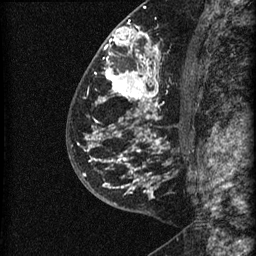
Breast MRI (dynamic contrast-enhanced), one sagittal slice. Slice 38 of 60 in the series (ordered by position). Dynamic contrast-enhanced series, image 2 of 3 at this slice position (ordered by acquisition). 1.5 T. TE 4.2 ms, TR 22.7 ms. 1.5 mm slice thickness. 256 × 256 image matrix. Female patient, age 48 years. From the clinical record (not read from this slice): setting: breast cancer imaged before/during neoadjuvant chemotherapy; receptor status: triple-negative.
Structures marked on this image (semi-automatically segmented with operator editing):
- analysis volume of interest (the breast-tissue region the enhancement analysis was run in; not a lesion): bounding box (x1, y1, x2, y2) in pixels: (81, 23, 186, 202)
- tumour enhancement mask (voxels above the 90 % enhancement threshold inside the analysis volume of interest): (83, 27, 160, 192)